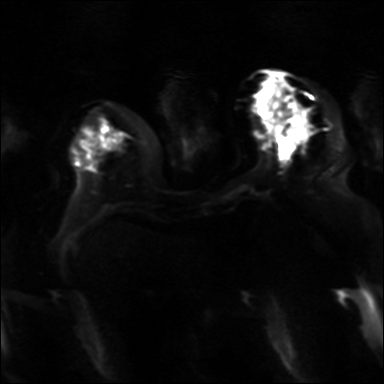
Breast MRI, one axial slice; slice 11 of 36 in the series (ordered by position); diffusion-weighted series; image 2 of 4 stored at this slice position (different b-values; order by instance number); 3 T; 4 mm slice thickness; 384 × 384 image matrix, field of view 320 × 320 mm. Female patient.
Outlined on this slice (outlined manually by an expert reader):
- tumour on diffusion-weighted imaging: box from (x=299, y=129) to (x=304, y=137) px